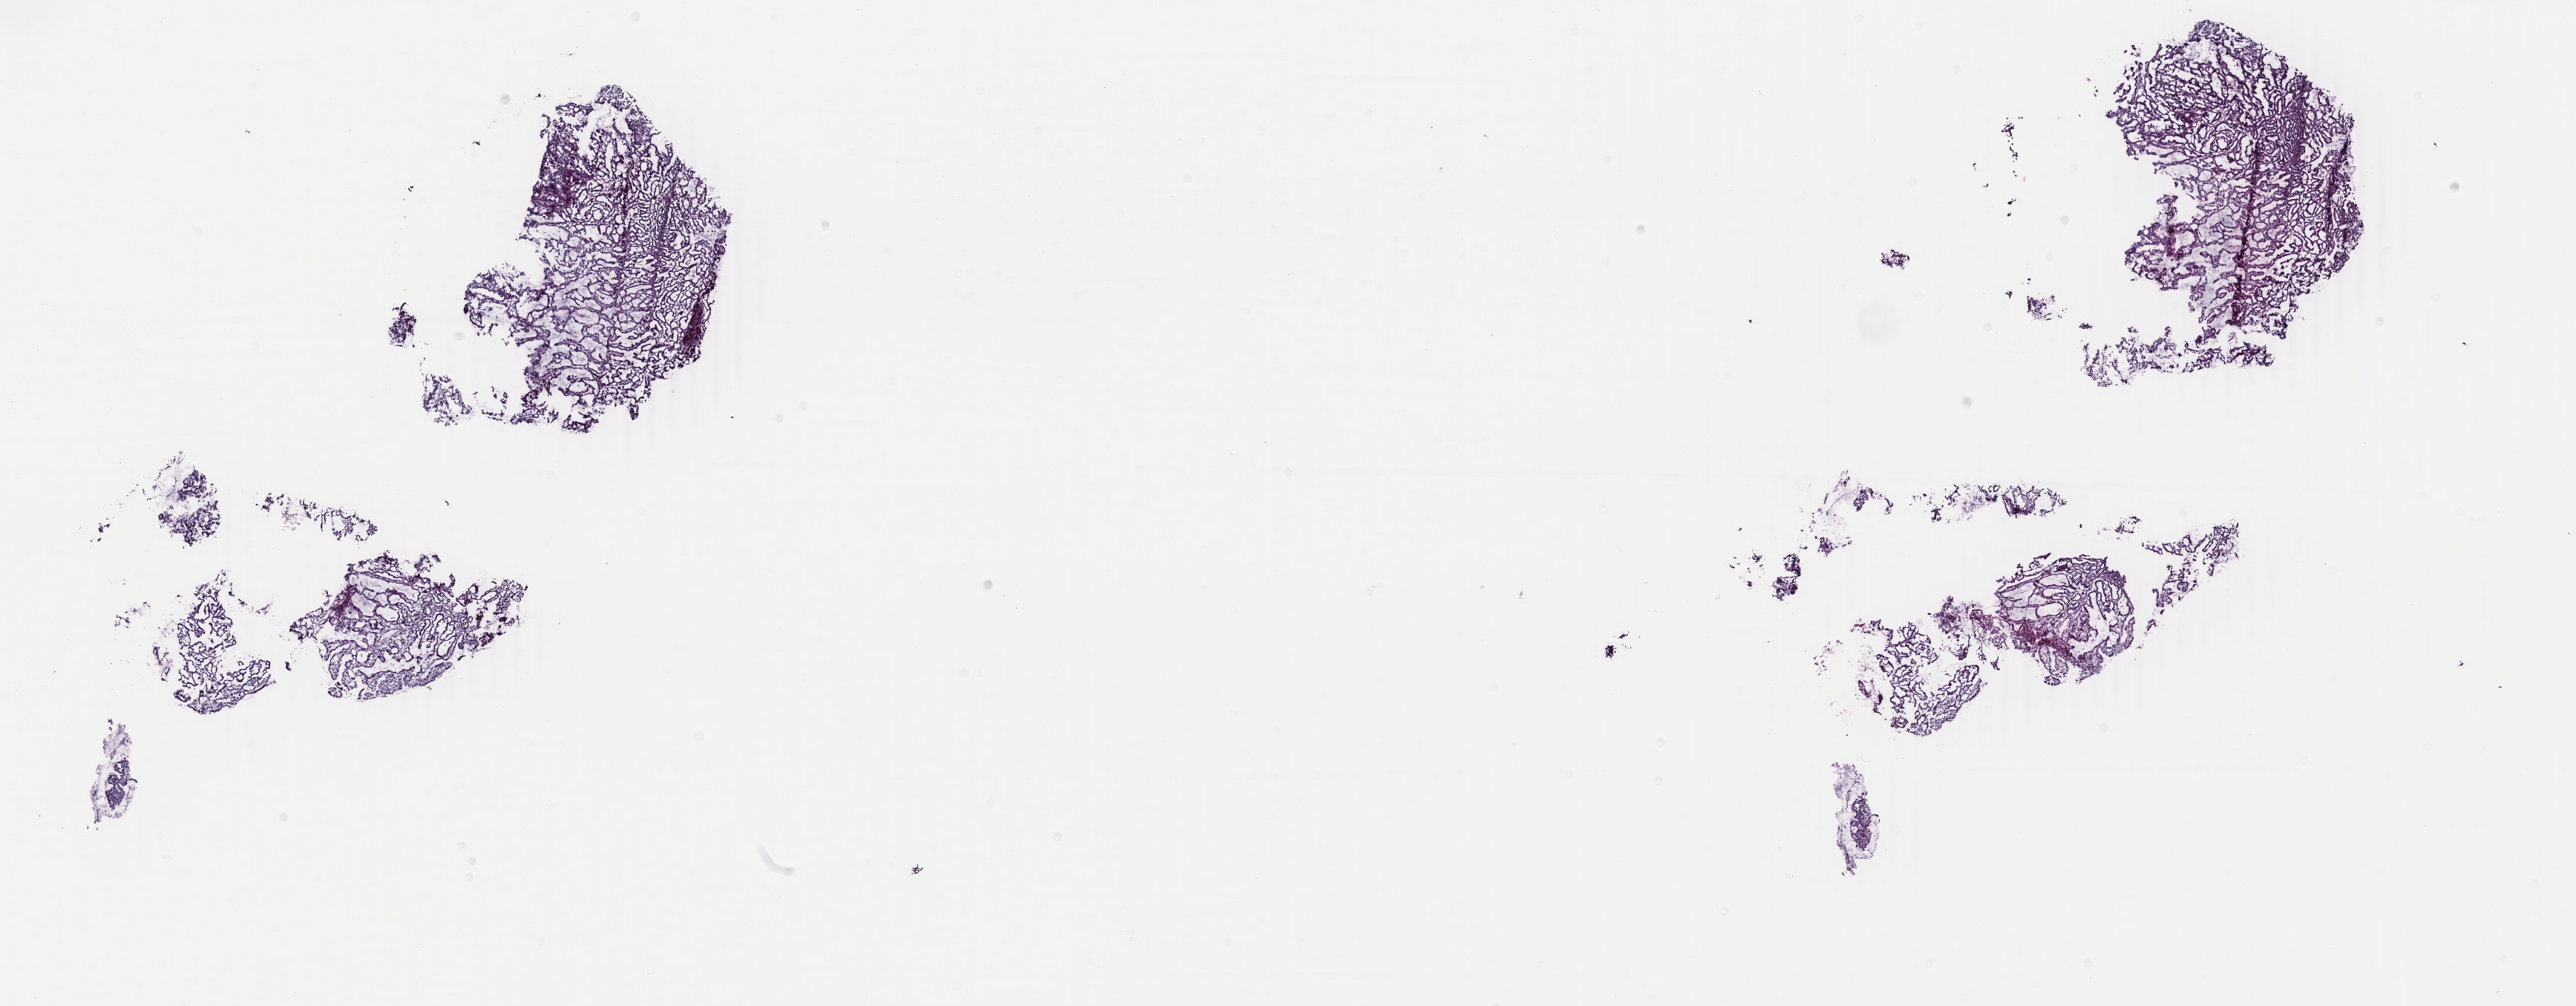
Whole-slide histology image, Hematoxylin and eosin (H&E) stained — shown as a low-resolution overview of the whole scanned area (about 27.6 x 10.8 mm, acquisition: 40x scan), frozen section from the top of the tissue portion, sample: primary tumour, uterus. Patient: female, age at initial diagnosis 54 years. Histologic grade: G1 (well differentiated). Composition of this section per pathologist review: tumour cells 100%, tumour nuclei 90%, normal cells 0%, stromal cells 0%, necrosis 0%. Inflammatory infiltration, as recorded: lymphocyte infiltration 0%, monocyte infiltration 0%, neutrophil infiltration 0%.
- FIGO stage: IIIA
- diagnosis: Endometrioid adenocarcinoma, NOS (endometrium)